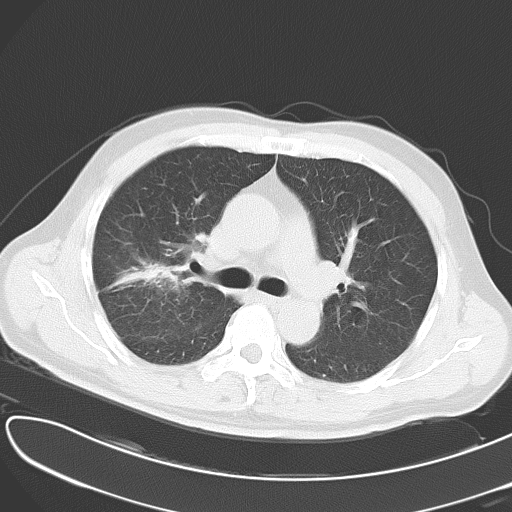
Chest CT, one axial slice; position 31 of 49 along the scan axis; reconstruction kernel B70f; 120 kVp; lung window (W 1500 / L -600 HU); 512 × 512 image matrix. Male patient, age 53 years. Case-level facts recorded for this patient, not image findings: clinical TNM (as recorded): T2 N1 M0.
Outlined on this slice (rectangle marked by the reading radiologist):
- lung tumour (recorded histology: adenocarcinoma): bounding box [x1, y1, x2, y2] px = [109, 257, 183, 293]